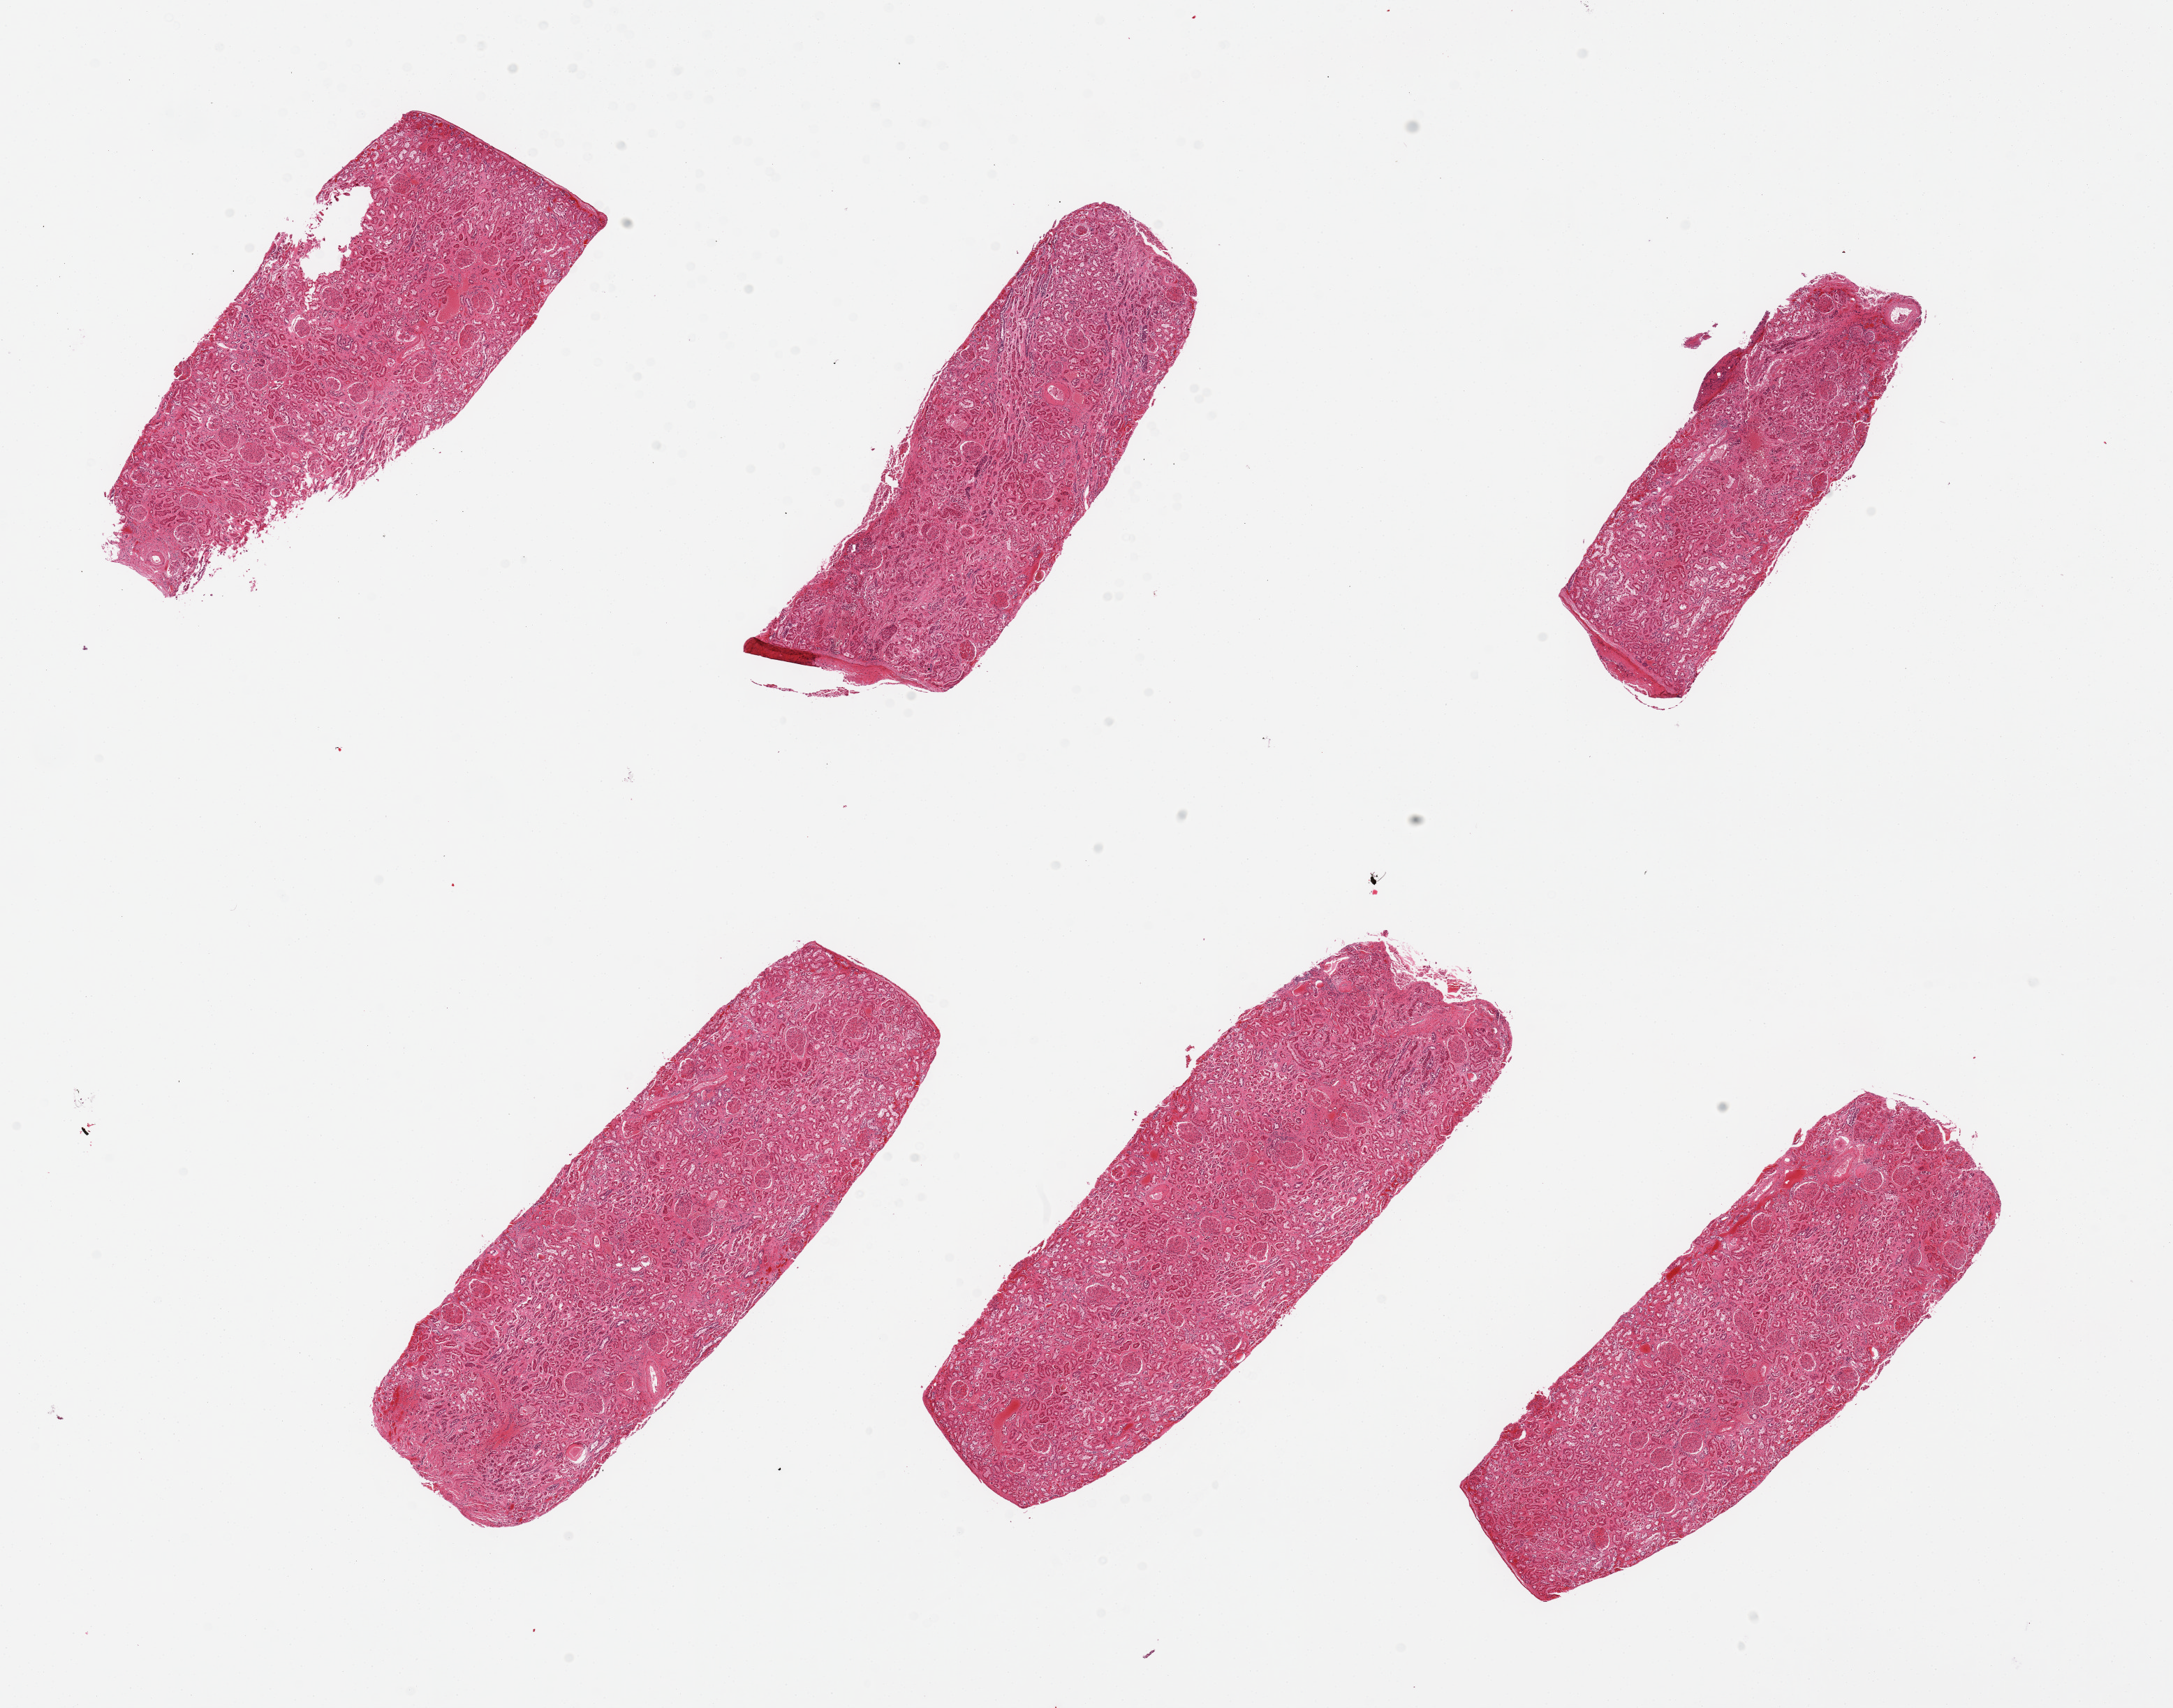
Whole-slide image, haematoxylin and eosin stain, a low-resolution overview of the entire scanned area, about 24.6 x 19.3 mm; PAXgene-fixed paraffin-embedded (PFPE) section; sampled site (target tissue): renal cortex; tissue donor sample. Donor: male.
Review note (as recorded): 6 pieces, glomeruli in all sections, arteriosclerosis.